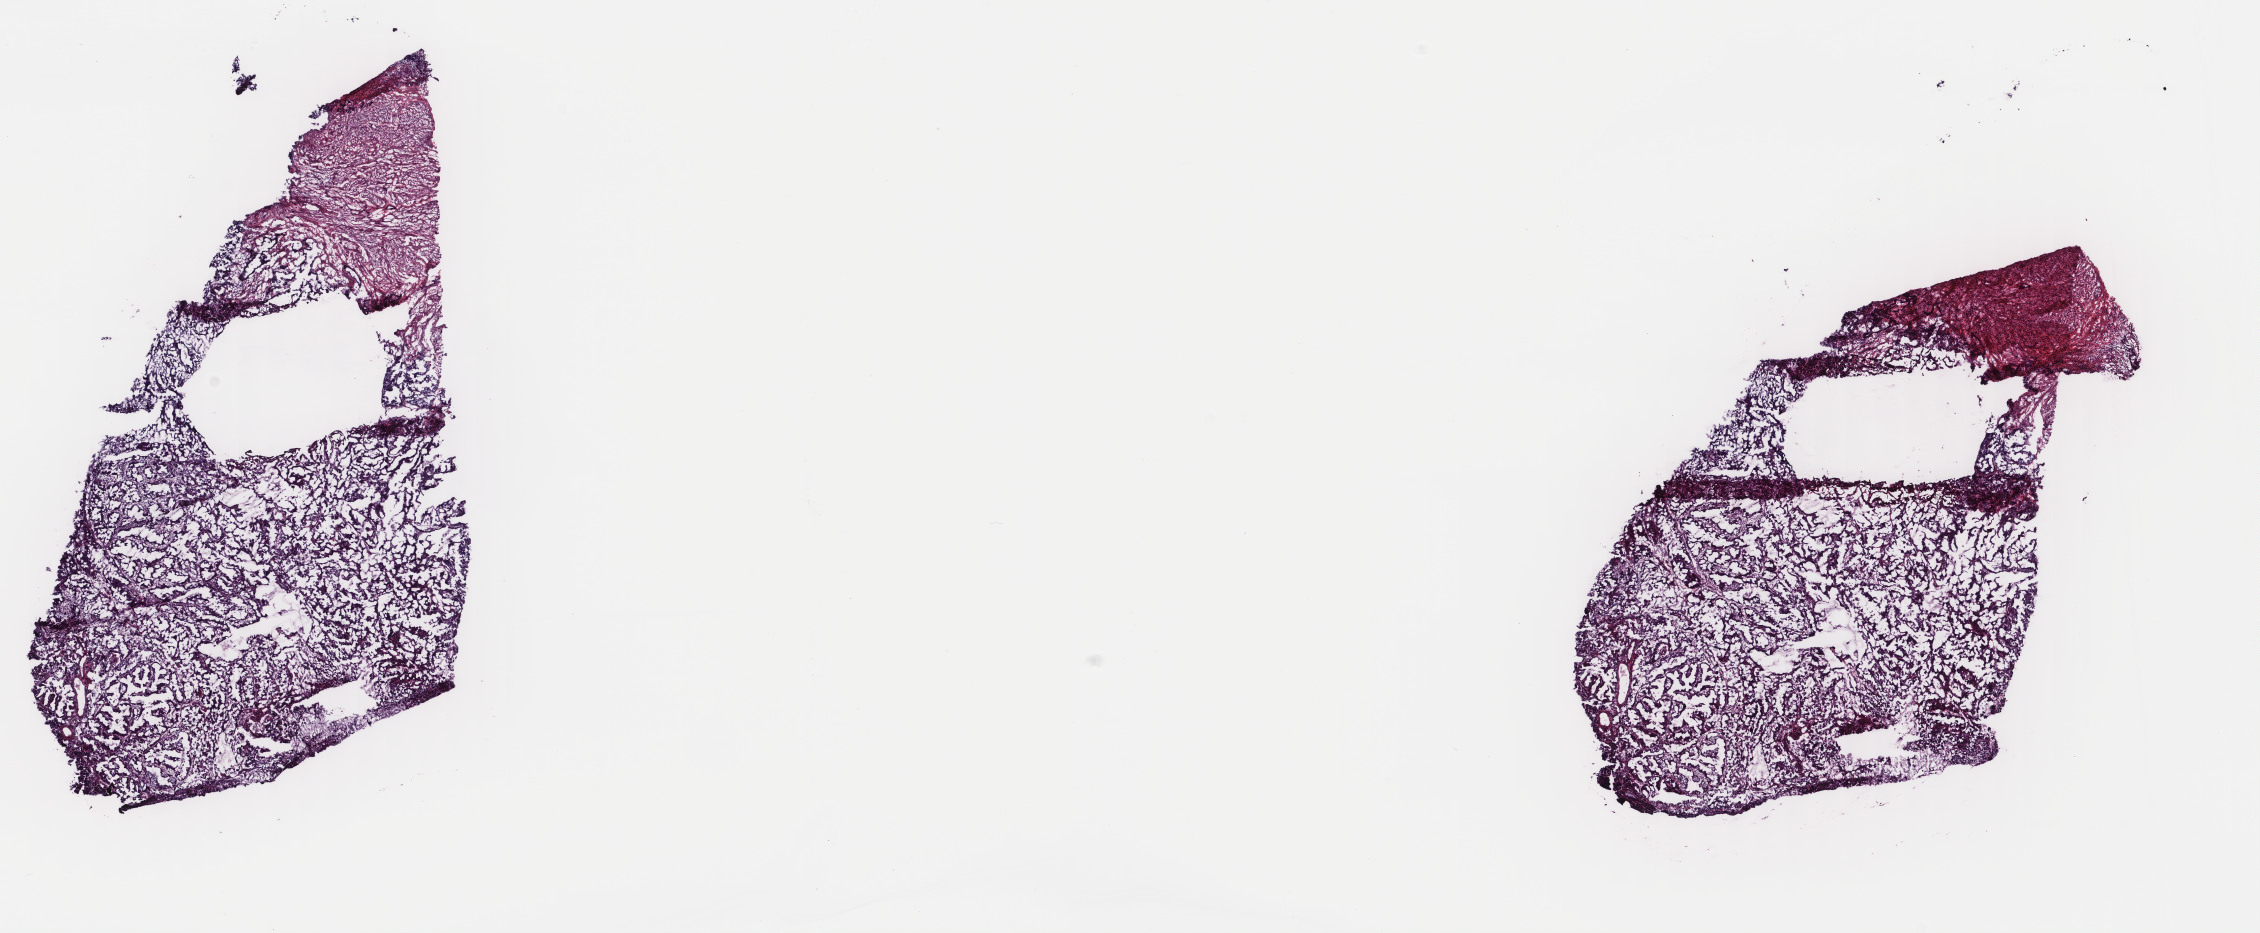
Digitized H&E tissue section (whole slide), low-resolution overview of the scanned area, about 17.9 x 7.4 mm (slide scanned at 40x). Frozen section from the top of the tissue portion. Sample: primary tumour, uterus. Female patient; age at initial diagnosis 69 years. Histologic grade: G3 (poorly differentiated). Slide review estimates, as recorded: tumour cells 80%, tumour nuclei 75%, normal cells 20%, stromal cells 0%, necrosis 0%. Inflammatory infiltration, as recorded: lymphocyte infiltration 0%, monocyte infiltration 0%, neutrophil infiltration 0%.
Pathologic diagnosis: Serous cystadenocarcinoma, NOS (endometrium). Lymph nodes positive (case pathology): 0 of 11 examined. FIGO stage: IA.